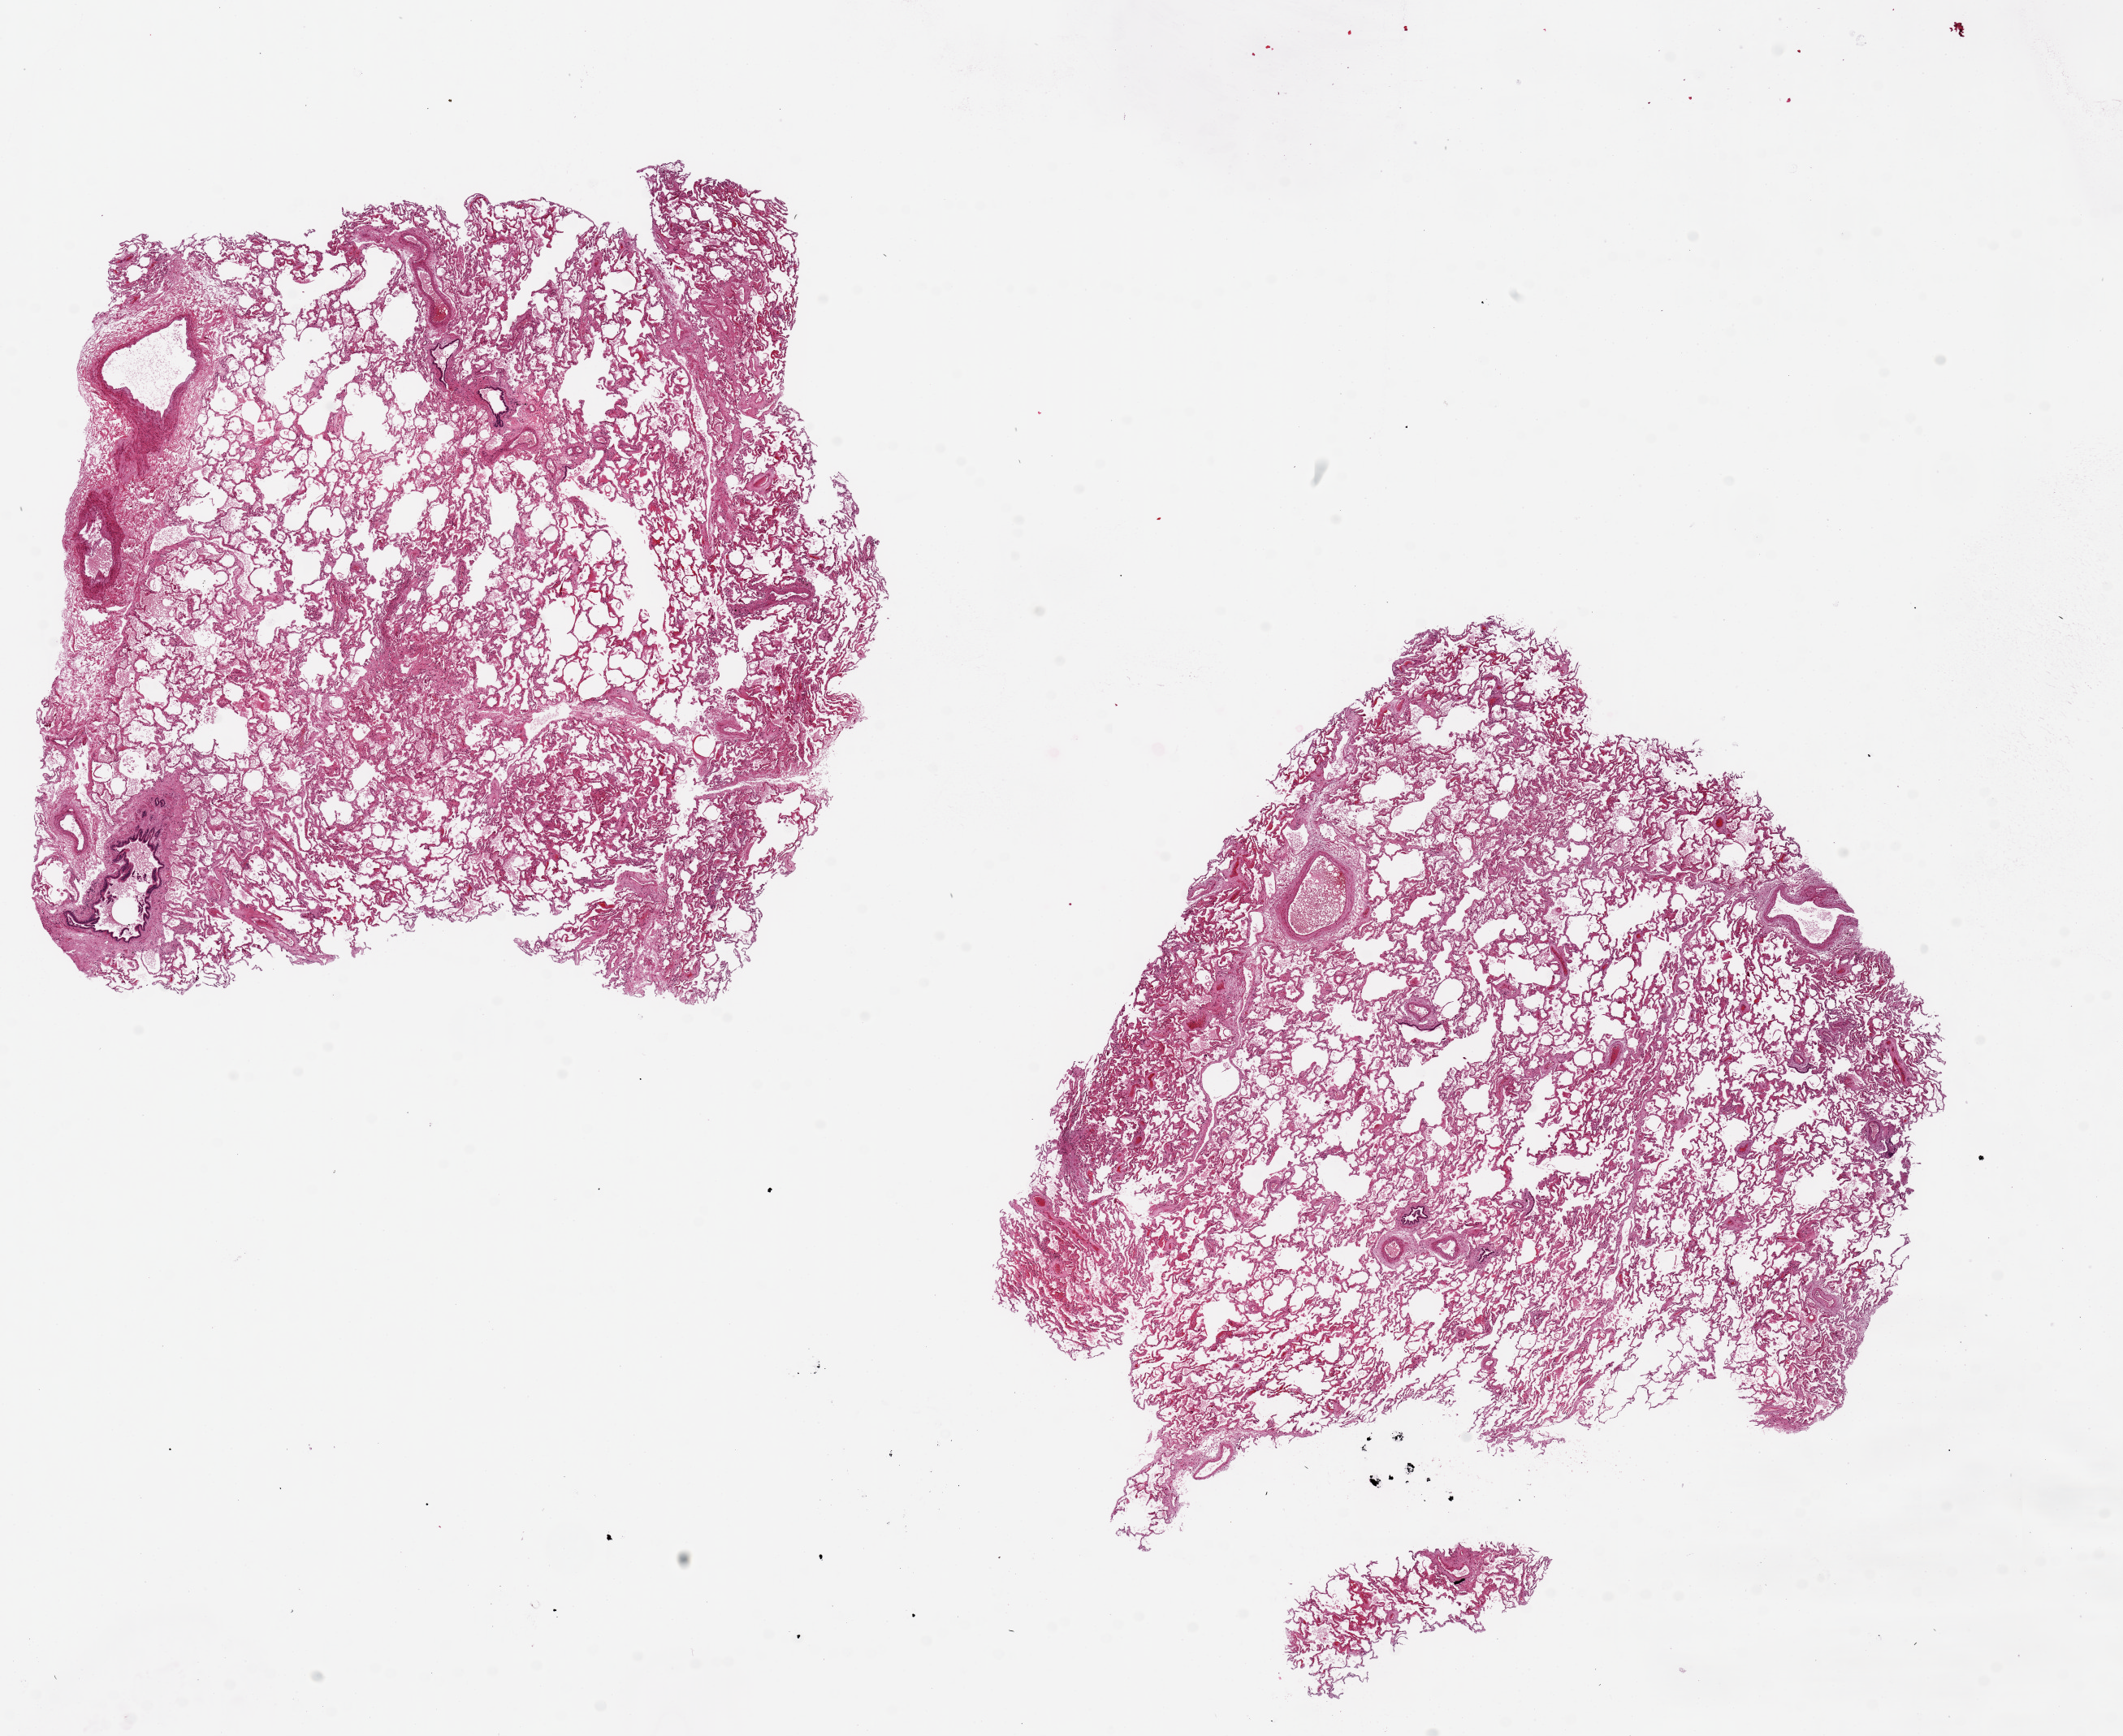
Whole-slide image, hematoxylin and eosin (H&E) stain — whole scanned area (about 20.7 x 16.9 mm) shown as a low-resolution overview; PAXgene-fixed, paraffin-embedded tissue; sampled site (target tissue): lung; tissue donor sample.
Reviewer comment on this tissue sample: 2 pieces ~8x8mm, minimal congestion.